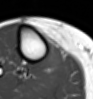
MRI of an extremity soft-tissue mass, one axial slice. Position 31 of 54 along the scan axis. MR volume resampled by the dataset authors to the PET/CT grid (not the native acquisition matrix). 3.27 mm slice thickness. 93 × 99 image matrix, field of view 91 × 97 mm. Female patient. Case-level facts recorded for this patient, not image findings: histological type: undifferentiated – high grade; grade: high; site of the primary tumour: right thigh.
Structures marked on this image (expert contour drawn on MRI and transferred to this co-registered scan by the dataset authors):
- gross tumour volume (mass): bounding box [x1, y1, x2, y2] px = [43, 45, 67, 72]